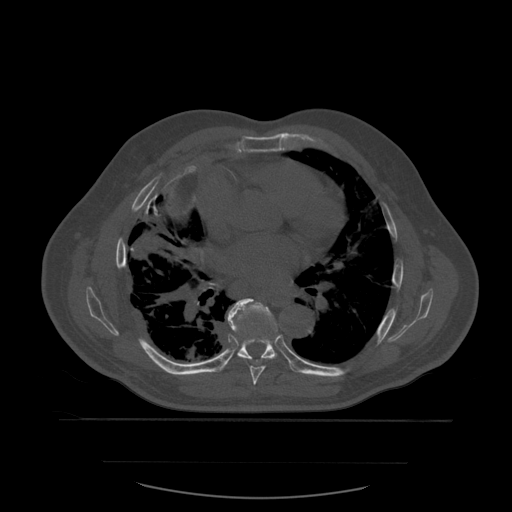
CT including the spine, one axial slice. Slice 374 of 590 in the series (ordered by position). Bone window (W 1800 / L 400 HU). 1.25 mm slice thickness. 512 × 512 image matrix, field of view 479 × 479 mm. Patient age 71 years. Case-level facts recorded for this patient, not image findings: primary cancer: lung.
Annotated regions visible in this slice (semi-automatic segmentation, software-assisted and operator-edited):
- T7 vertebra: box from (x=232, y=298) to (x=278, y=385) px
- T8 vertebra: (x=228, y=299)–(x=278, y=362)